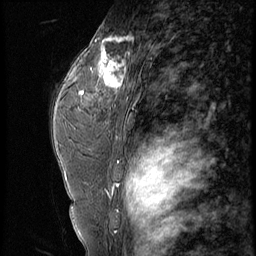
Breast MRI (dynamic contrast-enhanced), one sagittal slice; position 39 of 56 along the scan axis; 4 images stored at this slice position (order not interpretable as contrast timing); 1.5 T; TE 4.2 ms, TR 9 ms; 2.5 mm slice thickness; 256 × 256 image matrix, field of view 180 × 180 mm. Patient: female, 44 years. From the clinical record (not read from this slice): setting: breast cancer imaged before/during neoadjuvant chemotherapy; receptor status: triple-negative.
Outlined on this slice (semi-automatically segmented with operator editing):
- analysis volume of interest (the breast-tissue region the enhancement analysis was run in; not a lesion): bounding box (x1, y1, x2, y2) in pixels: (87, 28, 132, 99)
- tumour enhancement mask (voxels above the 140 % enhancement threshold inside the analysis volume of interest): (95, 37, 131, 94)